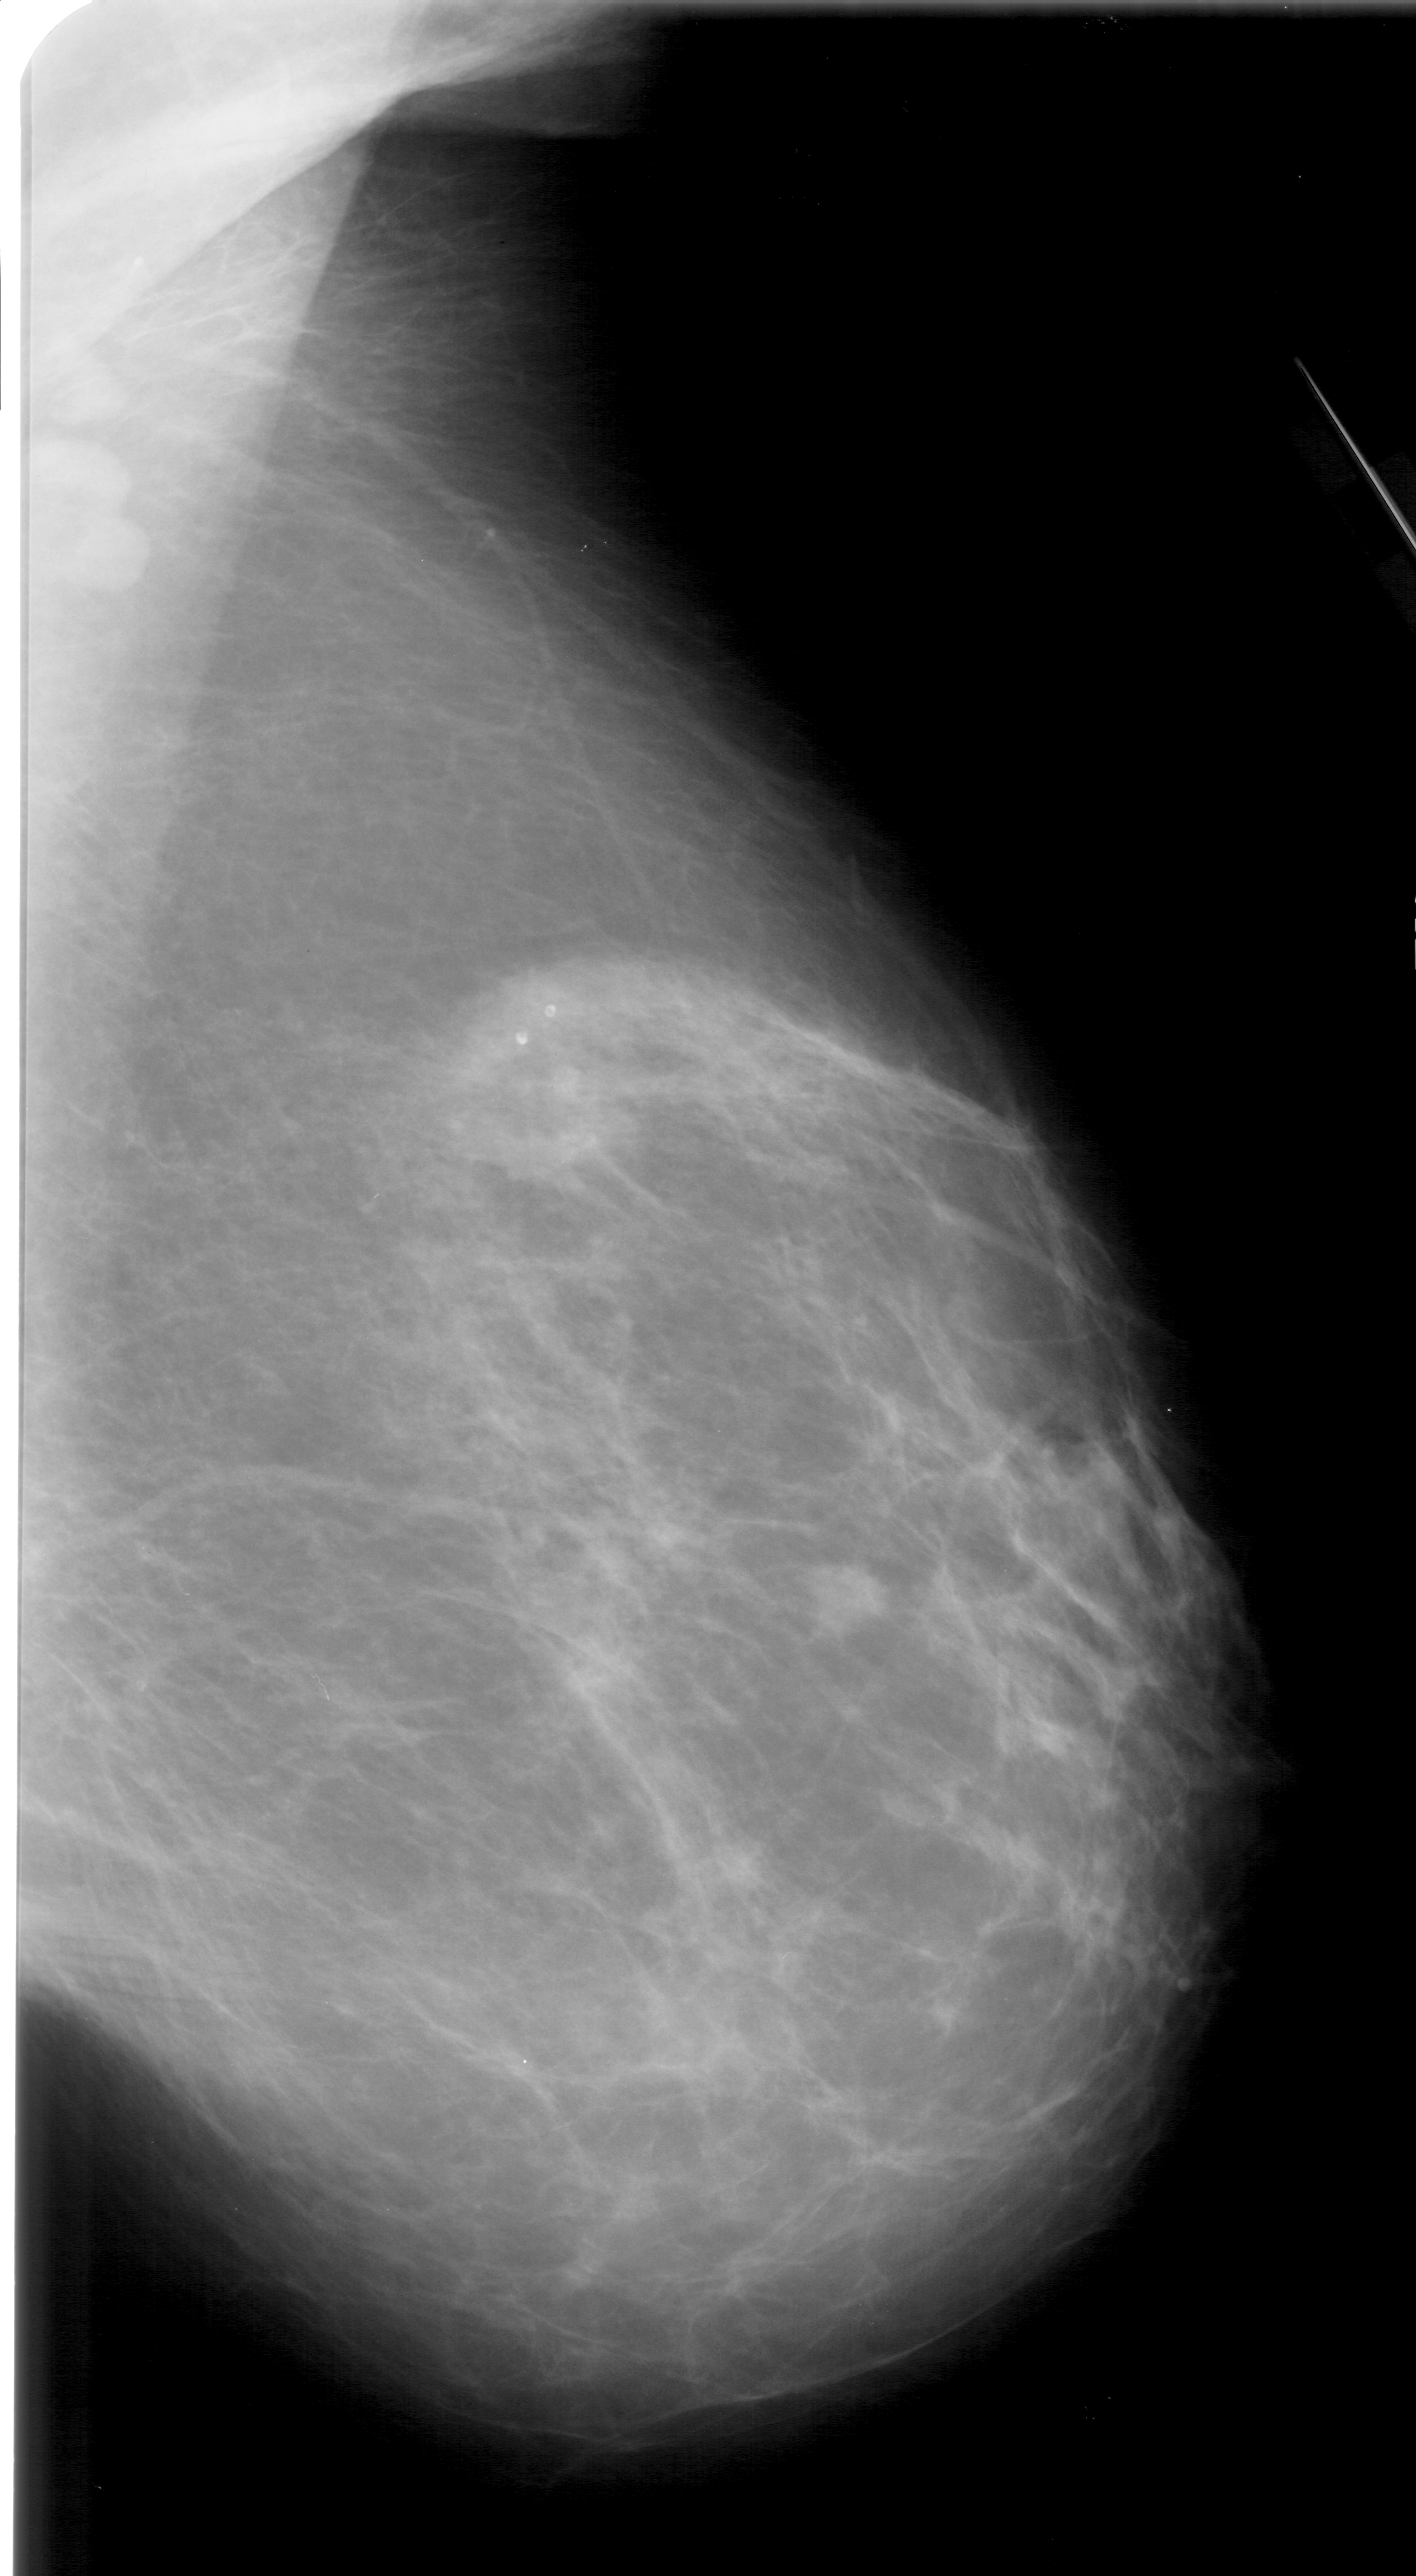
Mammogram (digitized film); right breast; MLO view; BI-RADS breast density category 2 (scale 1–4).
Mass, shape irregular, margins ill defined; BI-RADS assessment category 5; pathology result (as recorded, not read from the image): malignant.